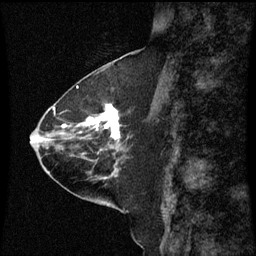
Breast MRI (dynamic contrast-enhanced), one sagittal slice; dynamic contrast-enhanced series, image 2 of 3 at this slice position (ordered by acquisition); 1.5 T; TE 4.2 ms, TR 8.9 ms; 2 mm slice thickness; 256 × 256 image matrix. Female patient, age 63 years. From the clinical record (not read from this slice): setting: breast cancer imaged before/during neoadjuvant chemotherapy; receptor status: HR-positive, HER2-negative.
Annotated regions visible in this slice (semi-automatic segmentation, software-assisted and operator-edited):
- analysis volume of interest (the breast-tissue region the enhancement analysis was run in; not a lesion): bounding box <77,102,131,151> (left, top, right, bottom; pixels)
- tumour enhancement mask (voxels above the 70 % enhancement threshold inside the analysis volume of interest): <85,104,120,139>